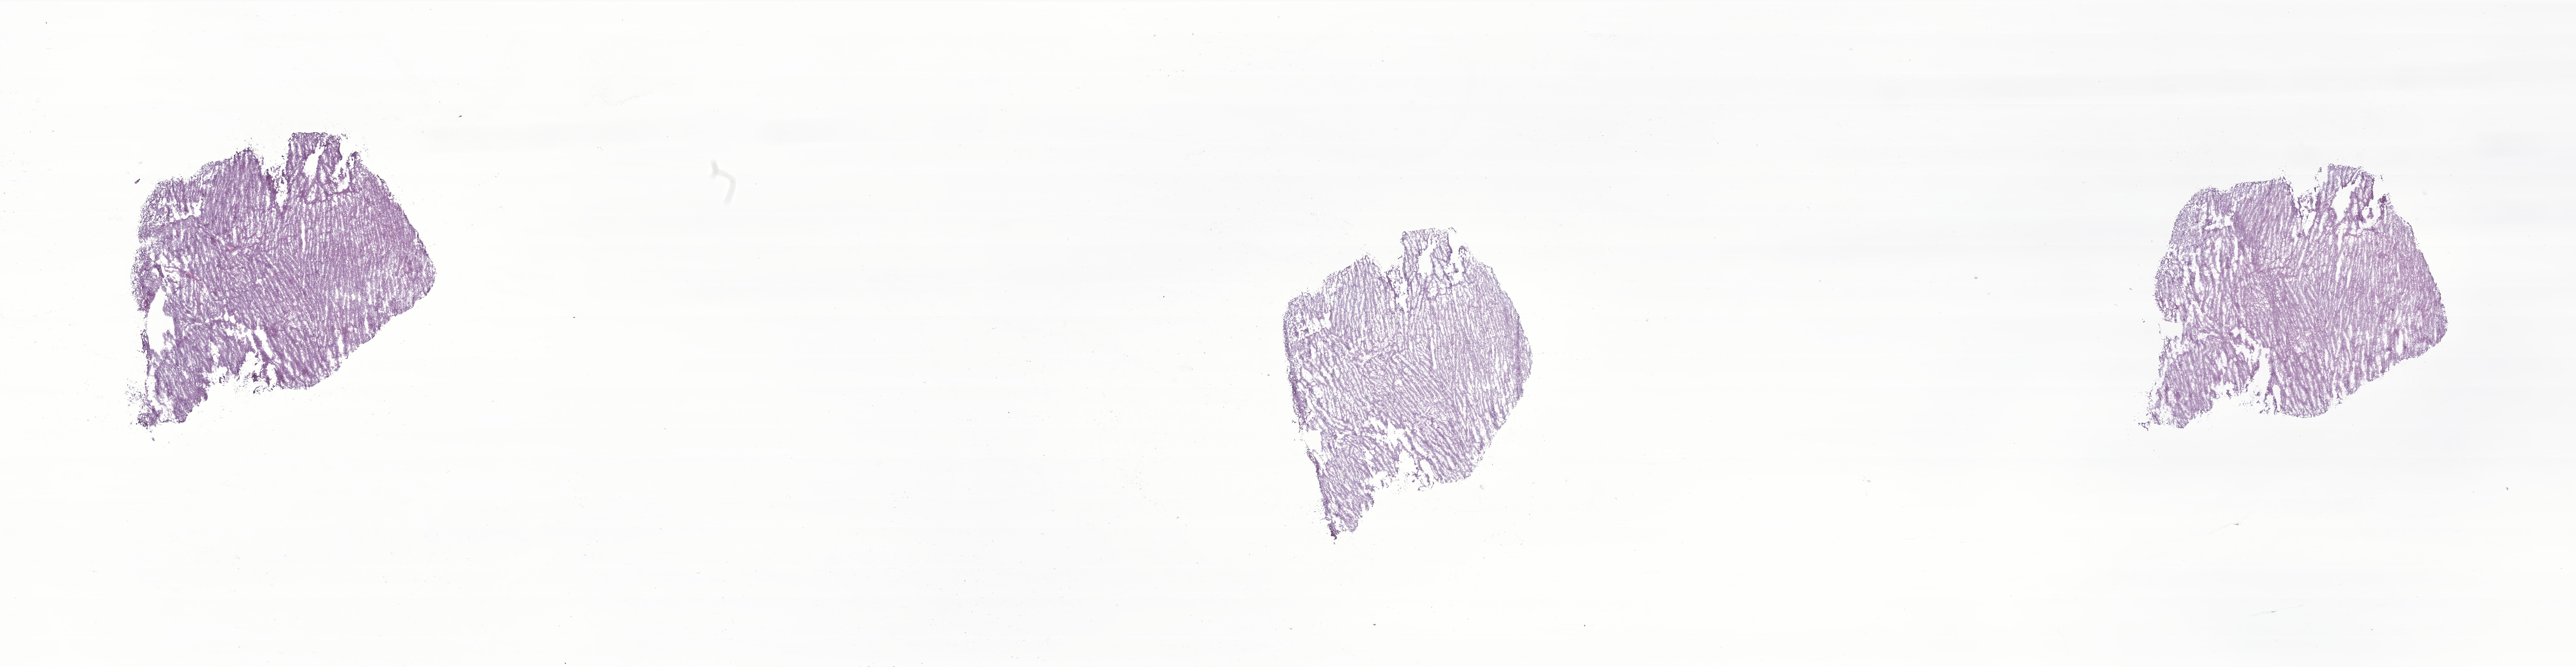
Haematoxylin and eosin whole-slide image of tumor tissue from the soft tissue — a low-resolution overview of the entire scanned area, about 39.0 x 10.1 mm; frozen section. Female patient, age 166 months (13 years 10 months).
Diagnosis (ICD-O-3 morphology term): Synovial sarcoma, spindle cell.